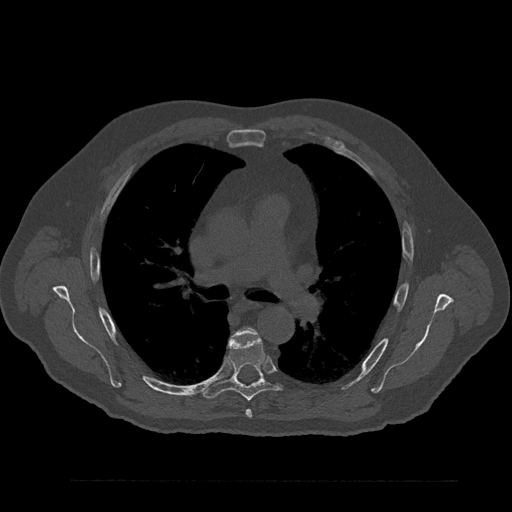
CT including the spine, one axial slice; position 563 of 797 along the scan axis; 120 kVp; bone window (W 1800 / L 400 HU); 512 × 512 image matrix, field of view 430 × 430 mm. Male patient, age 61 years. From the clinical record (not read from this slice): primary cancer: prostate.
Annotated regions visible in this slice (semi-automatically segmented with operator editing):
- T5 vertebra: bounding box (x1, y1, x2, y2) in pixels: (237, 328, 256, 418)
- T6 vertebra: (203, 337, 284, 401)